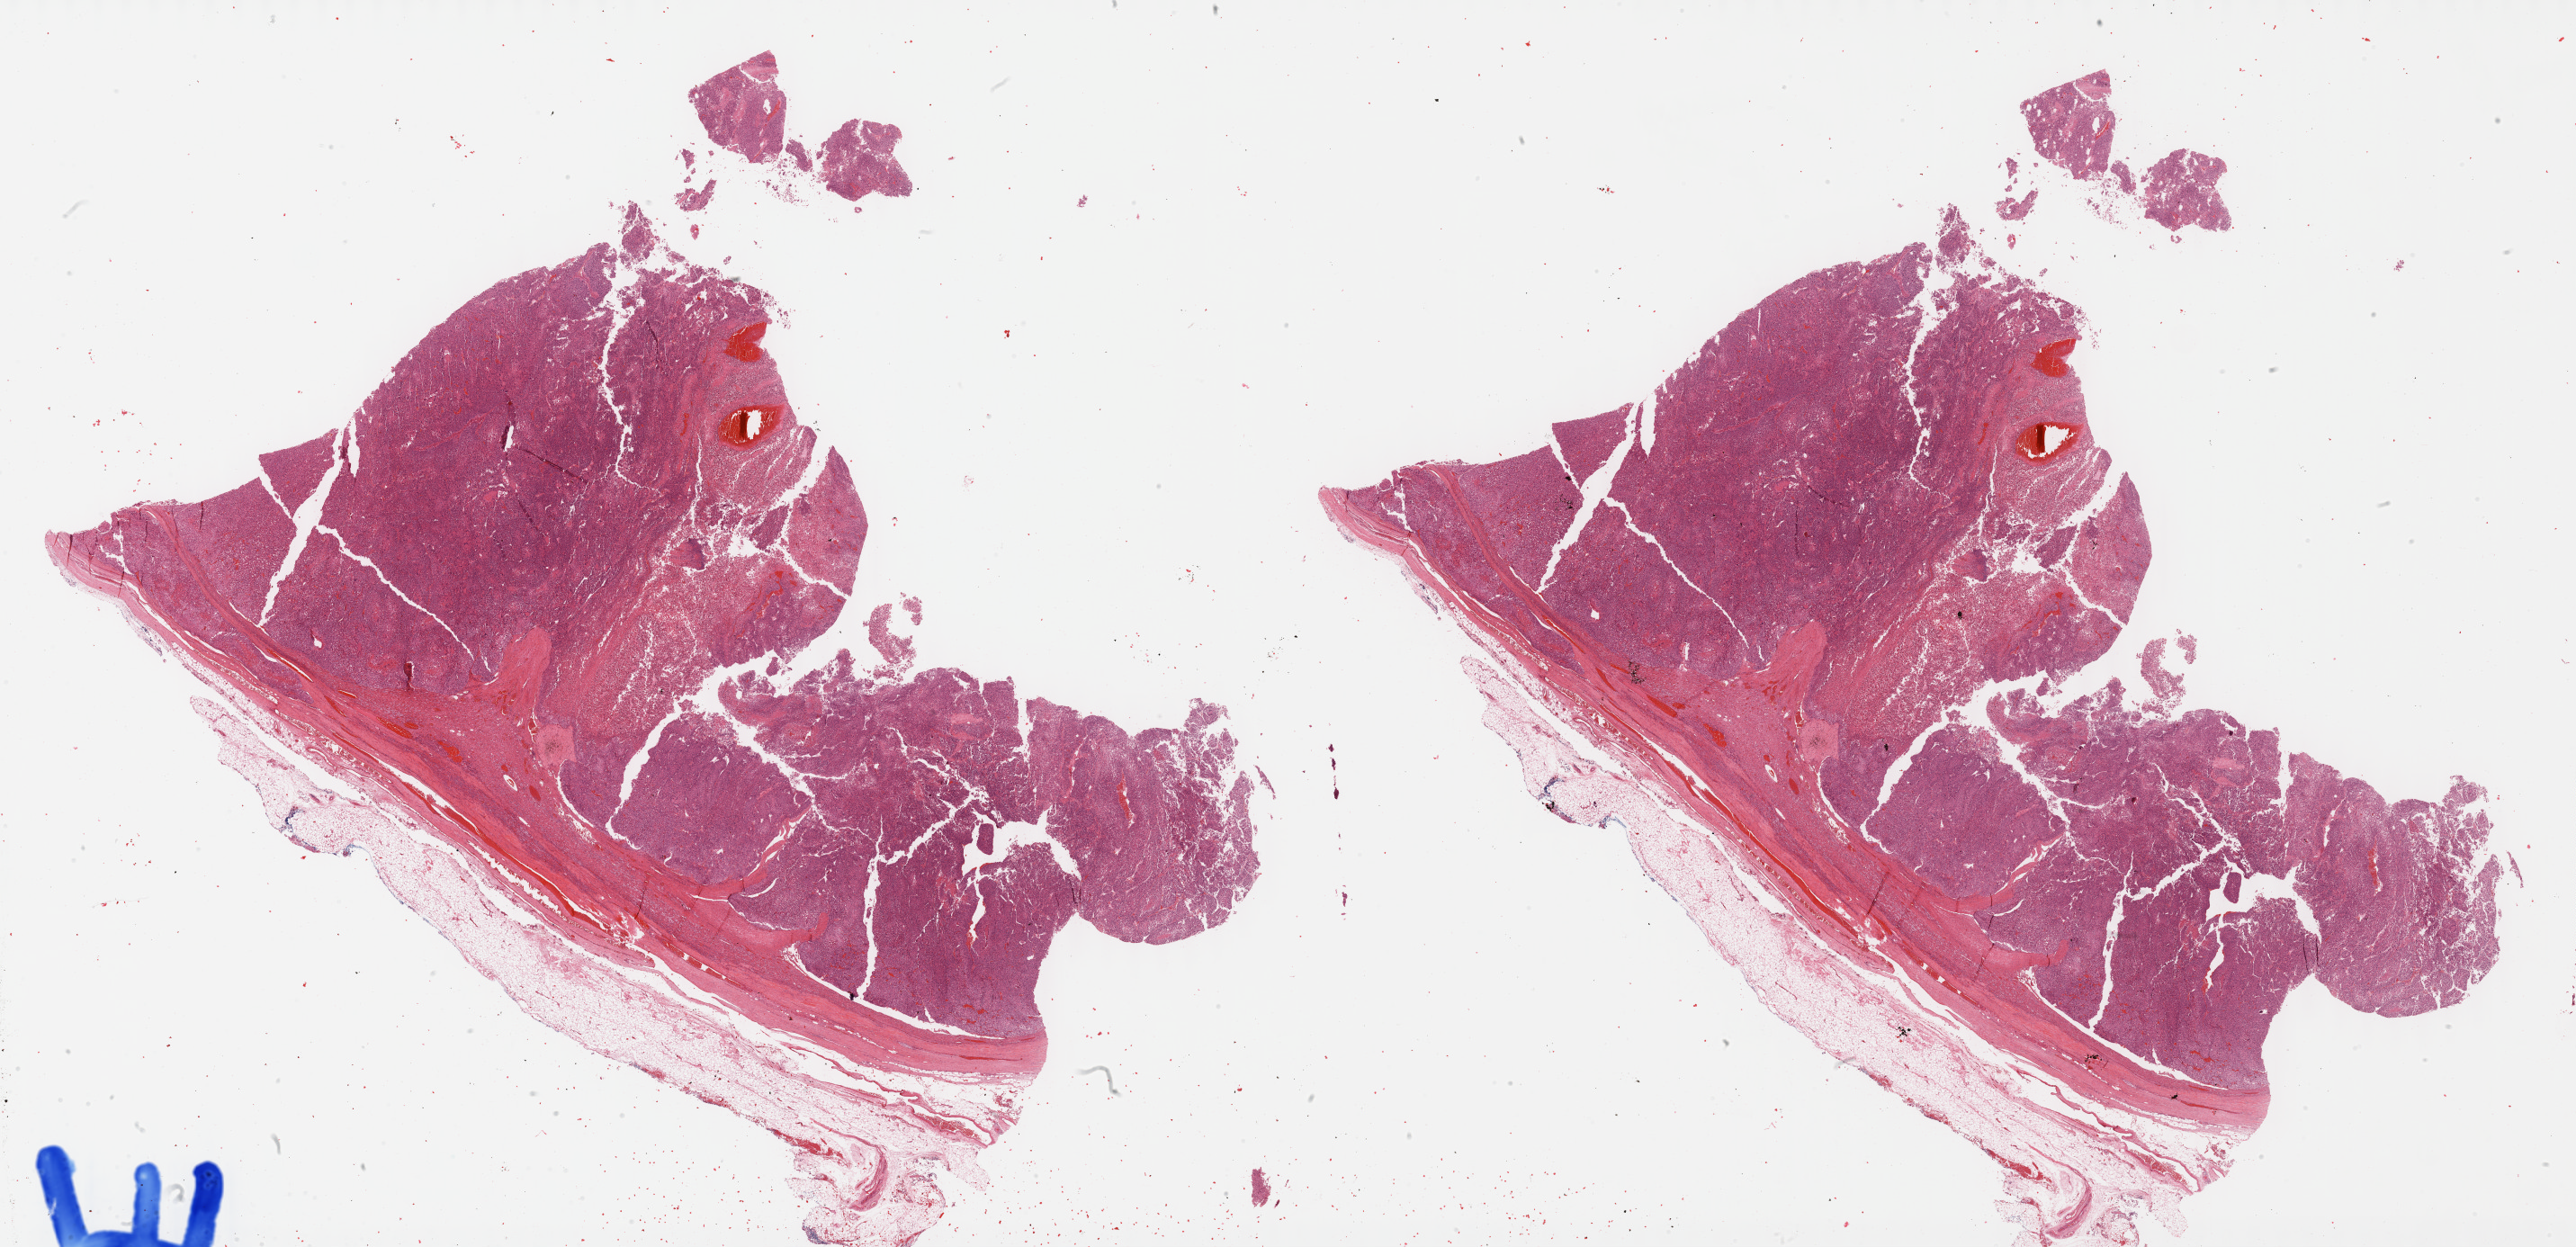
Whole-slide histology image, Hematoxylin and eosin (H&E) stained — low-resolution overview of the scanned area, about 46.3 x 22.4 mm; formalin-fixed paraffin-embedded (FFPE) diagnostic section; adrenal cortex, primary tumour sample. Female patient; age at initial diagnosis 53 years.
• pathologic diagnosis: Adrenal cortical carcinoma (cortex of adrenal gland)
• laterality: right